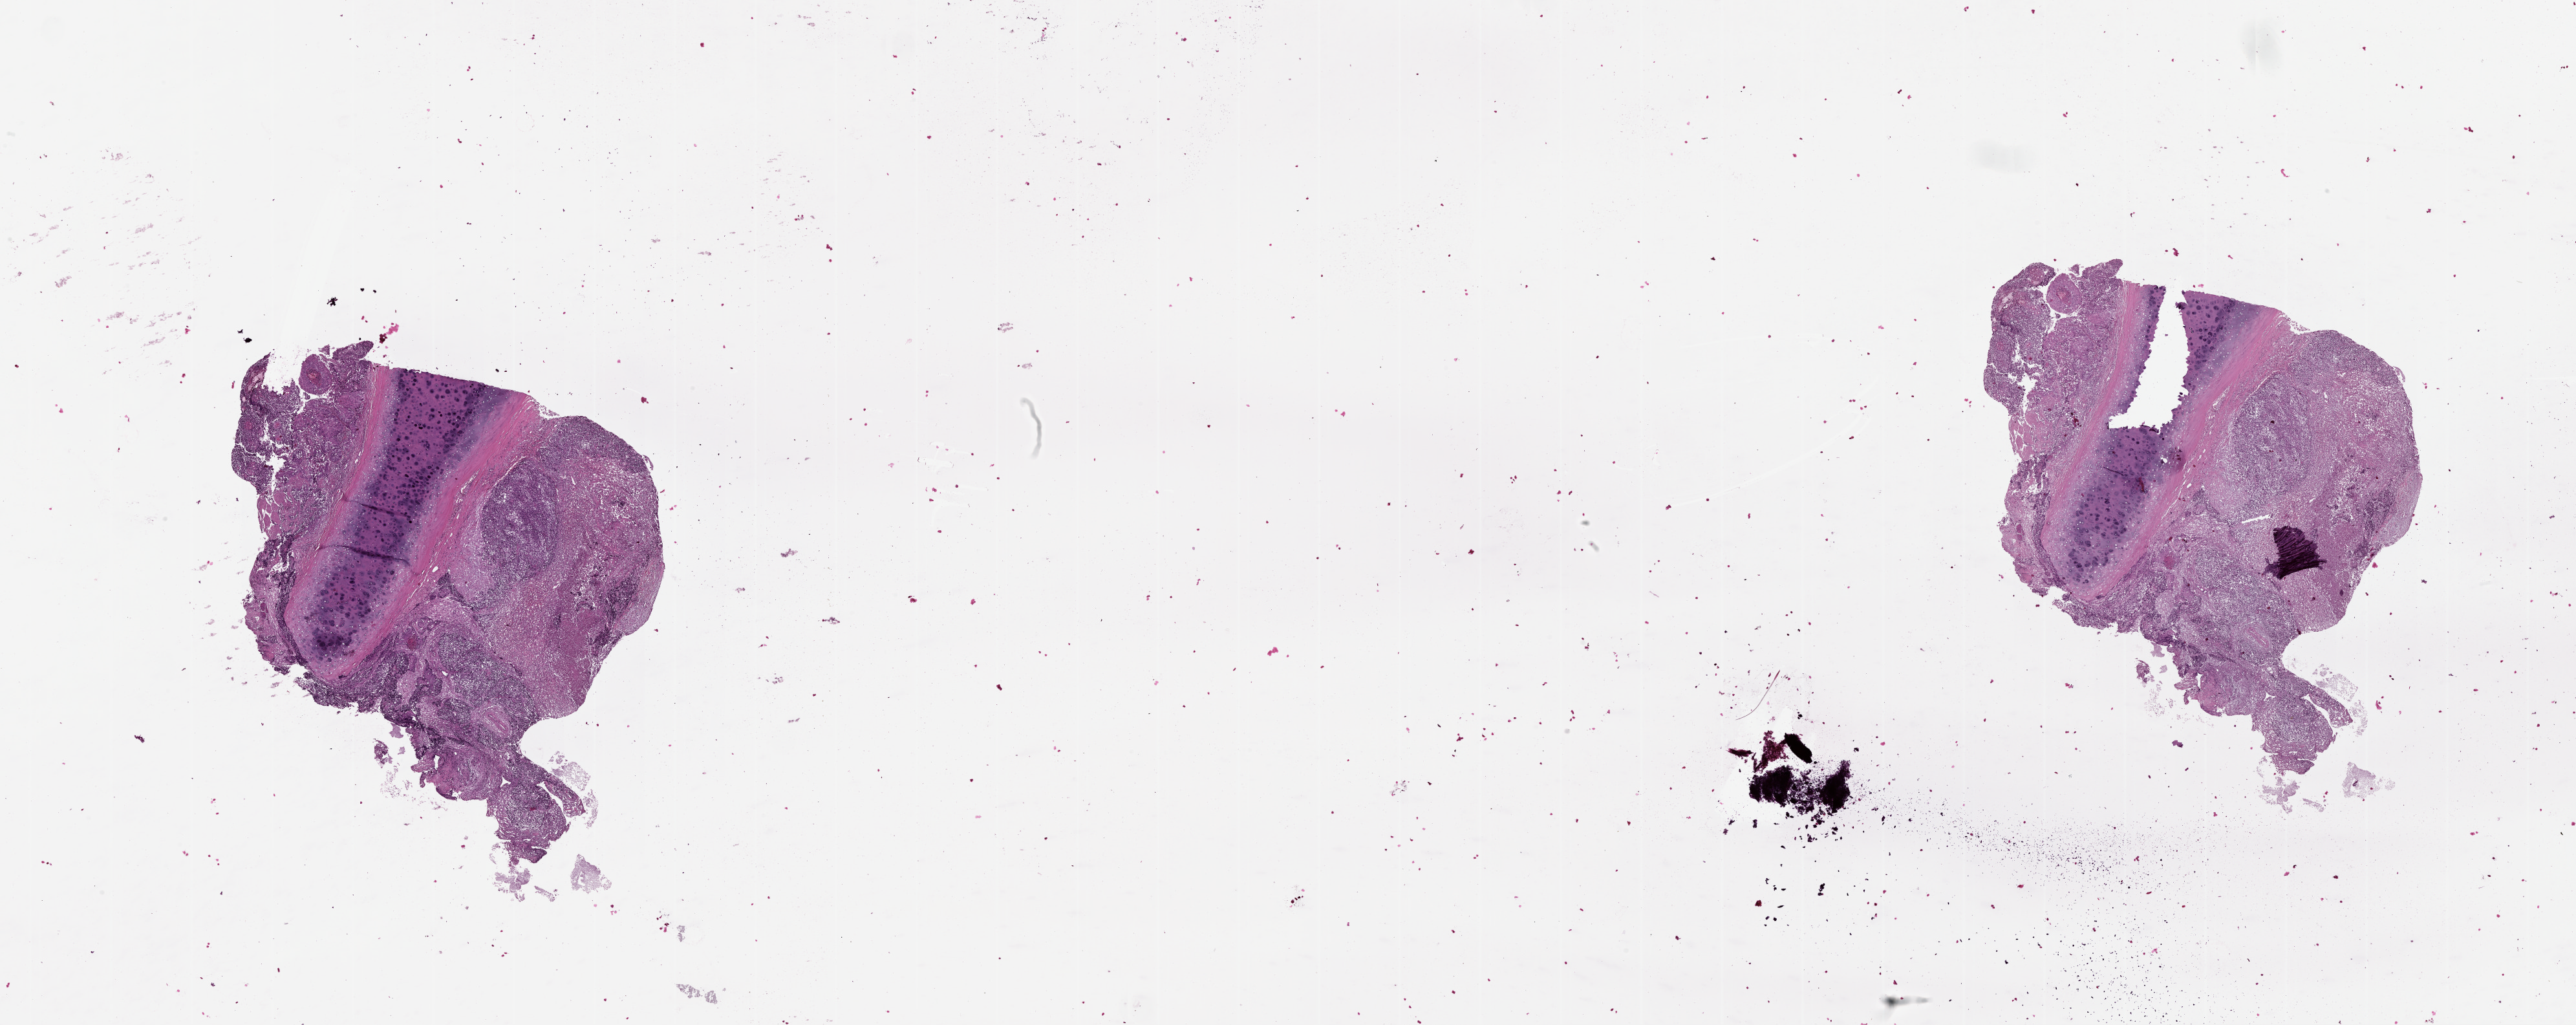
Whole-slide histology image, H&E-stained — whole scanned area (about 32.1 x 12.8 mm) shown as a low-resolution overview; lung, tumour tissue. Patient: male, age 65 years.
- patient diagnosis (cohort enrolment): squamous cell carcinoma (lung)